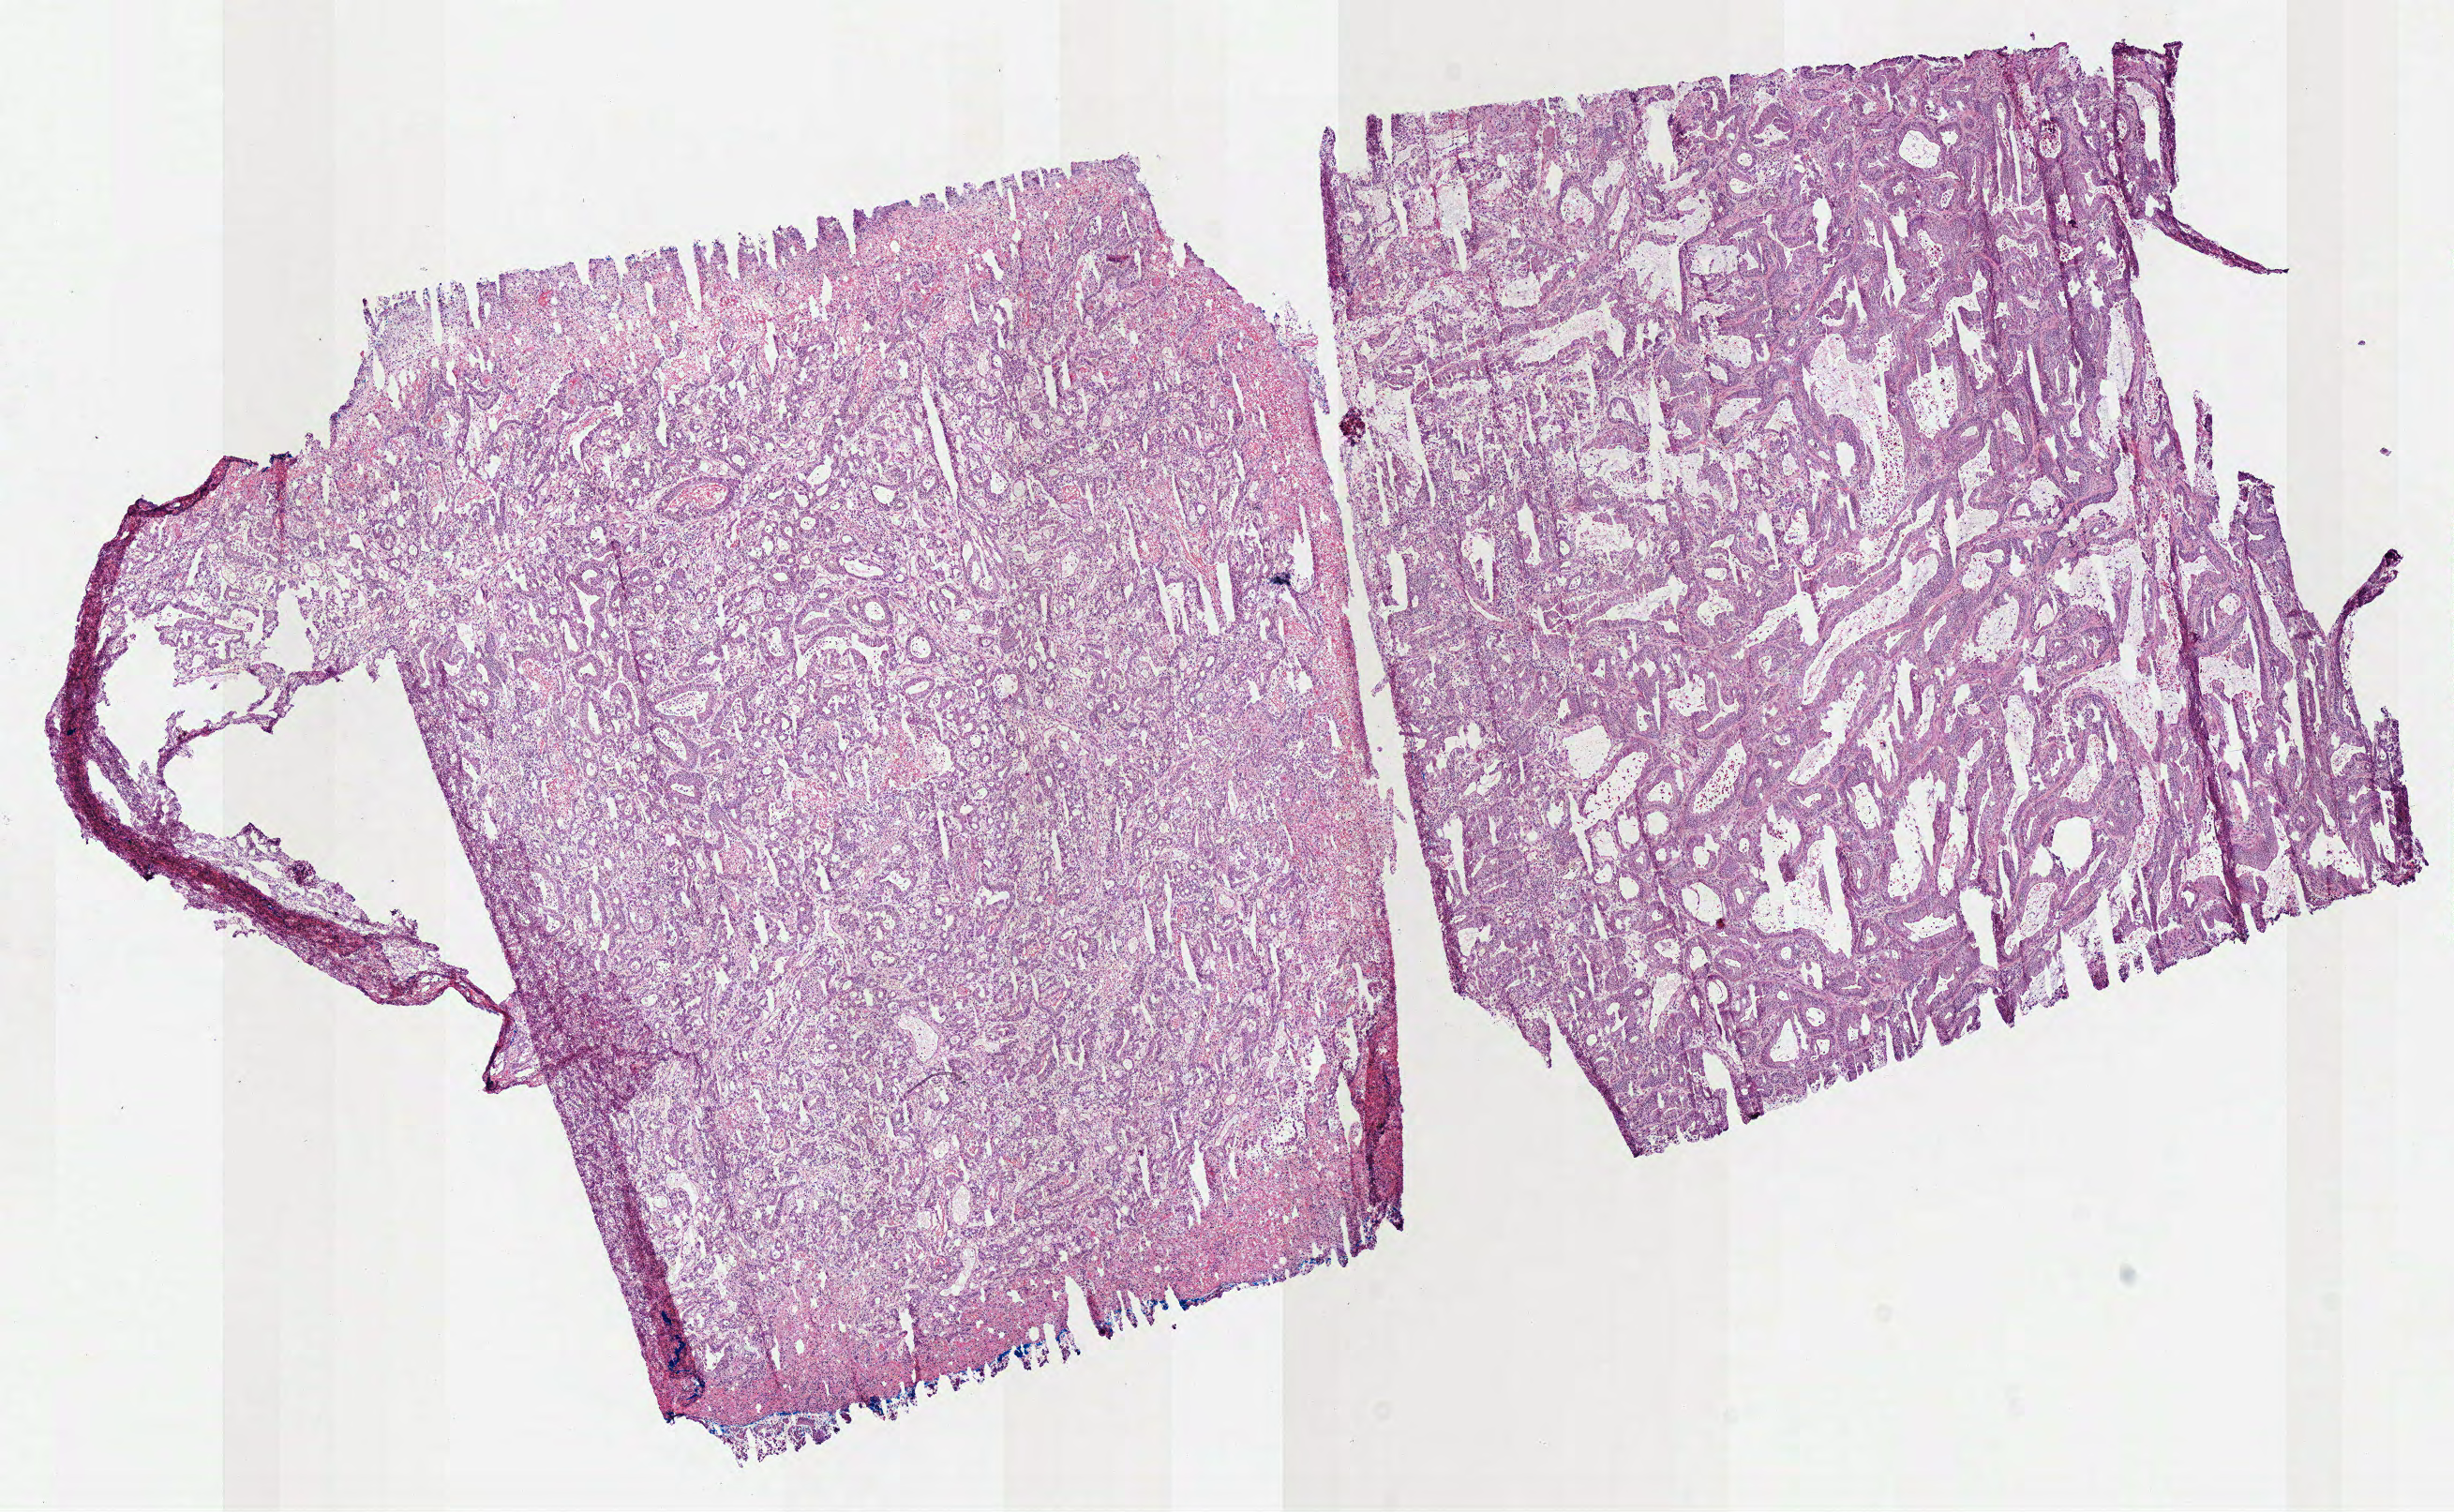
H&E whole-slide image — shown as a low-resolution overview of the whole scanned area (about 10.3 x 6.4 mm, from a 40x scan); frozen section from the top of the tissue portion; stomach, primary tumour sample. Male, age 79 years at initial diagnosis. Histologic grade: G3 (poorly differentiated). Composition of this section per pathologist review: tumour cells 85%, tumour nuclei 85%, normal cells 0%, stromal cells 10%, necrosis 5%. Infiltration values recorded for this section: lymphocyte infiltration 2%, neutrophil infiltration 3%.
Lymph nodes positive (case pathology): 0 of 38 examined. Histologic diagnosis: Adenocarcinoma, intestinal type (cardia, NOS). AJCC pathologic stage: IB (7th edition).